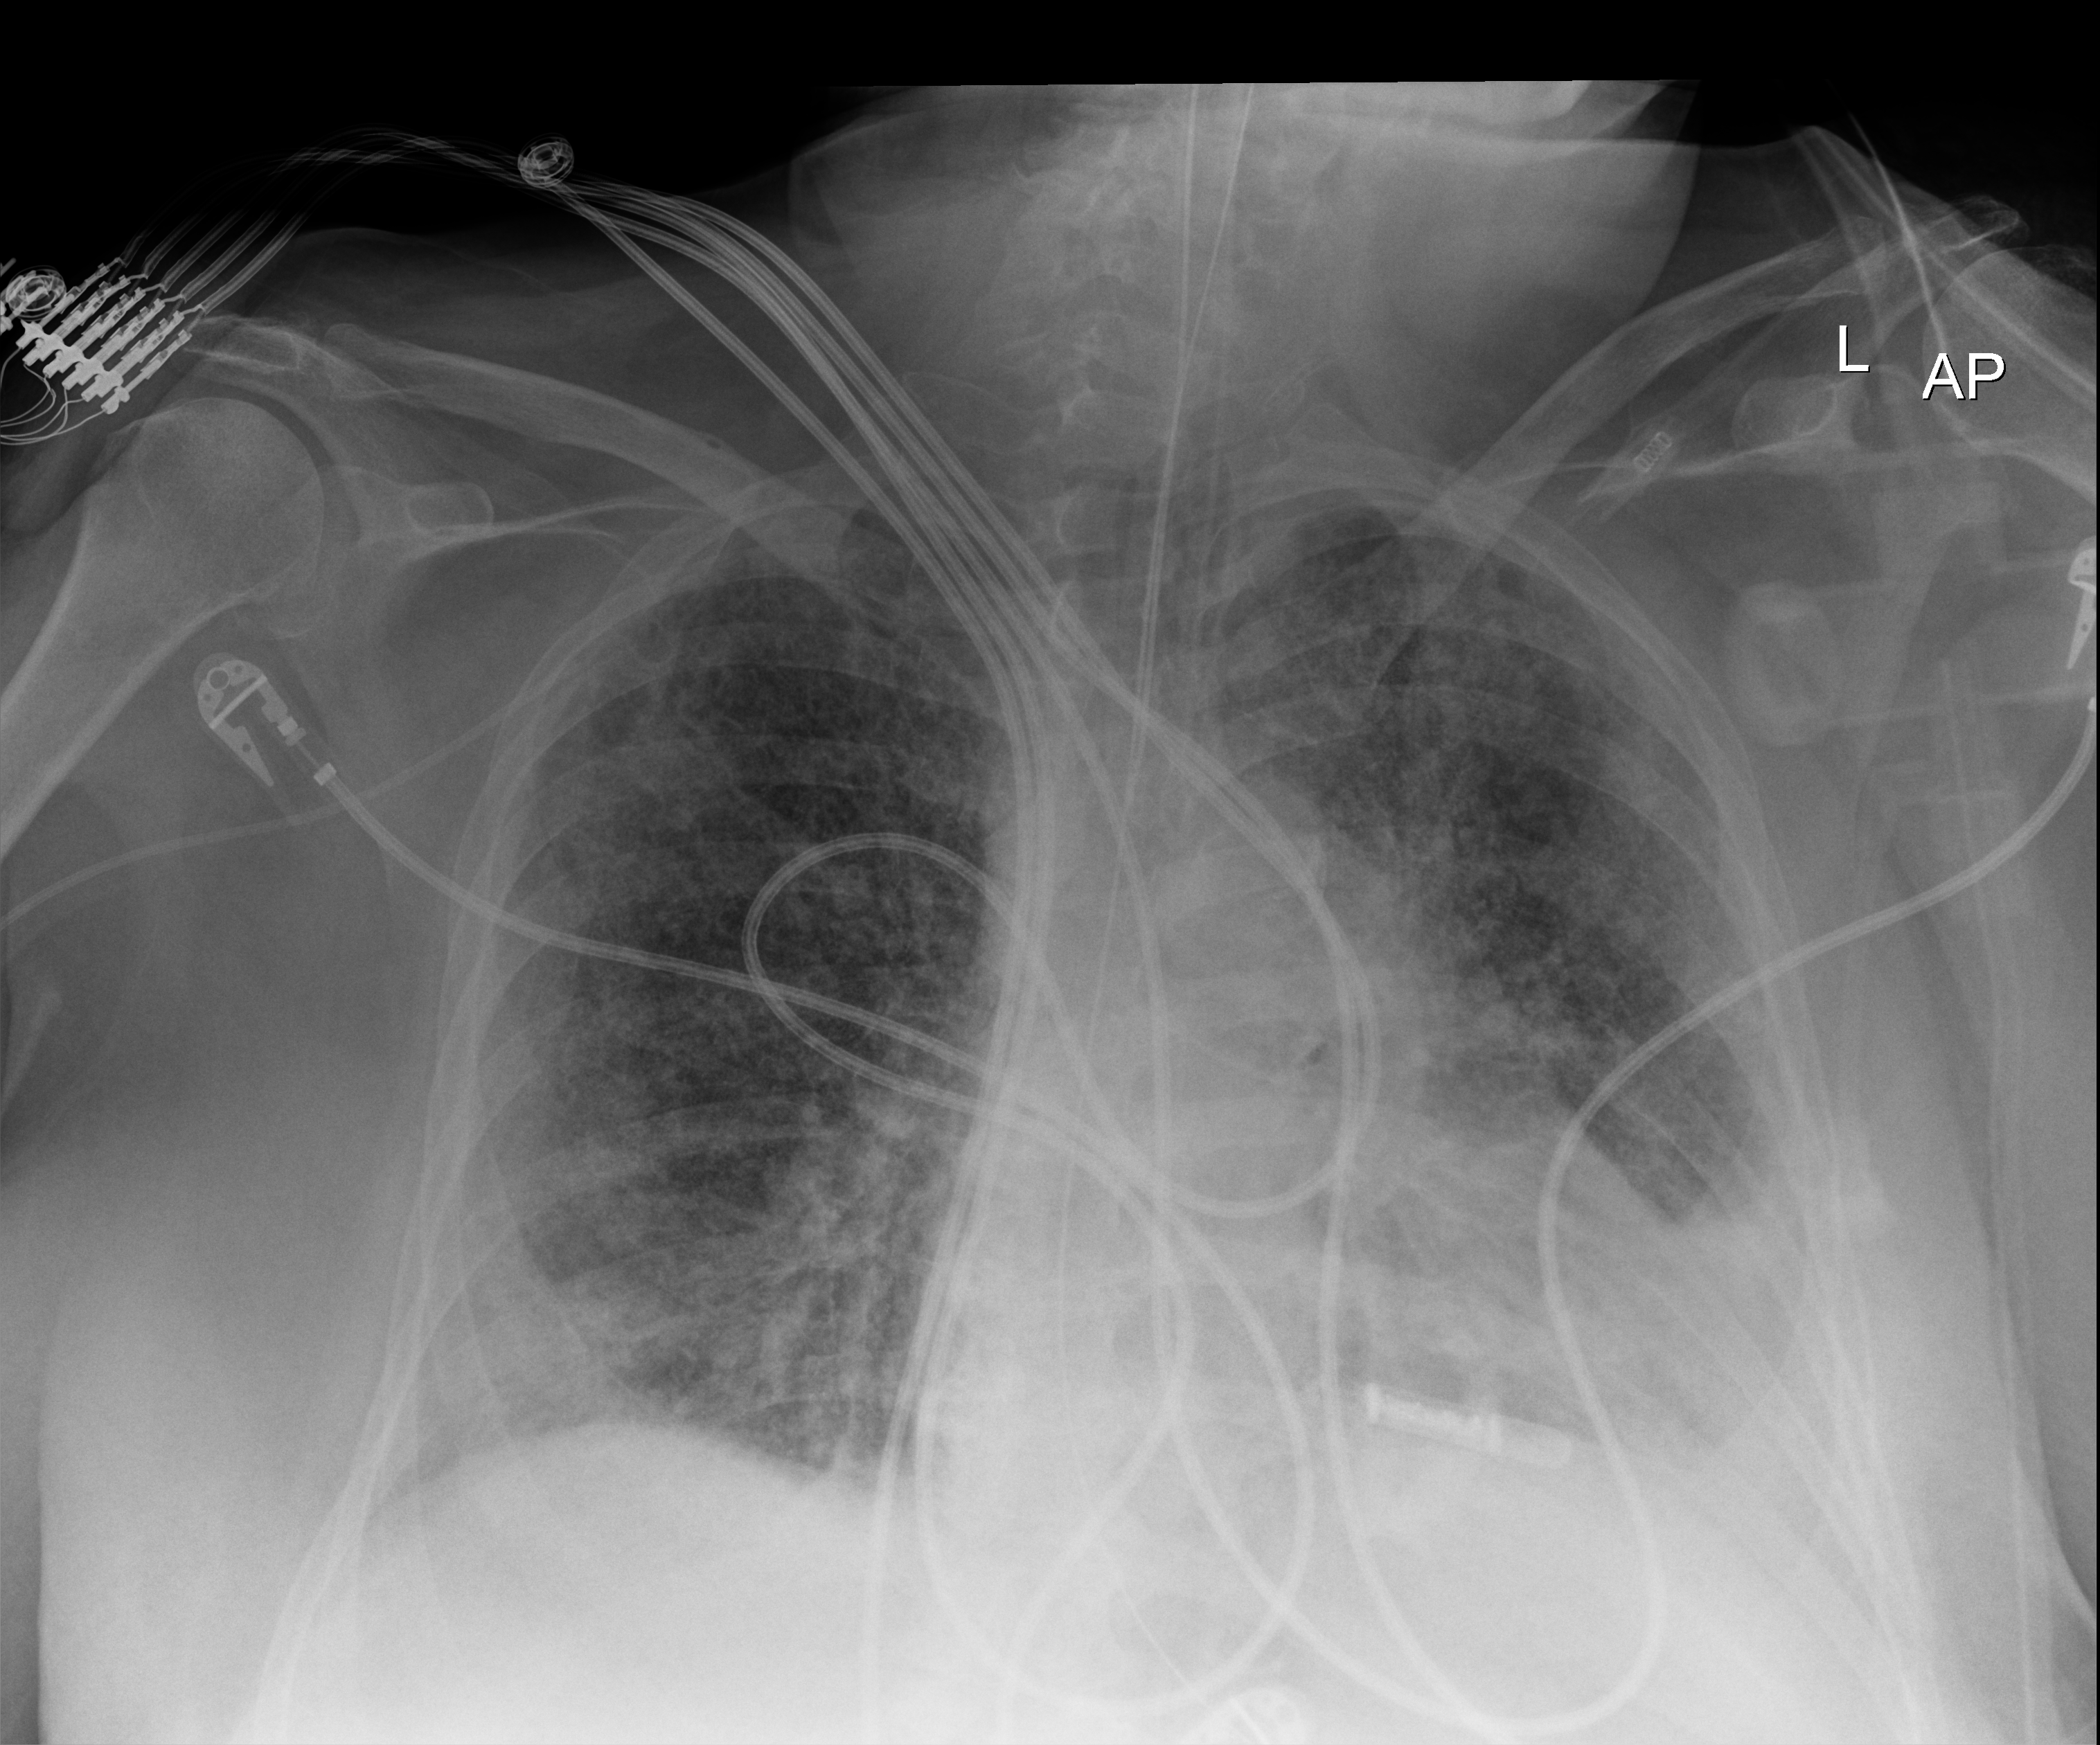
Portable chest radiograph, anteroposterior (AP) projection. Female patient hospitalised with COVID-19, age 60–74 years.
Admission-level facts for this patient (not findings on this image; timing relative to this image not recorded):
- mechanically ventilated during this hospital stay: yes
- length of hospital stay: 28 days
- admitted to intensive care during this hospital stay: yes